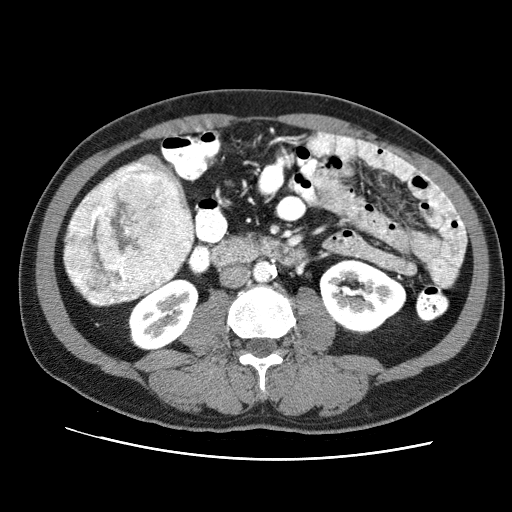
Contrast-enhanced abdominal CT (liver protocol), one axial slice. Position 17 of 71 along the scan axis. Reconstruction kernel STANDARD. Soft-tissue window (W 400 / L 40 HU). 2.5 mm slice thickness. 512 × 512 image matrix, field of view 360 × 360 mm. Case-level facts recorded for this patient, not image findings: diagnosis: hepatocellular carcinoma (patient treated with transarterial chemoembolisation; whether this scan precedes or follows treatment is not stated here); TNM stage (as recorded): Stage-II; Child-Pugh class: A.
Structures marked on this image (semi-automatically segmented with operator editing):
- liver parenchyma outside the tumour (the mass and vessels are separate outlines, so this box may not span the whole liver): bounding box <67,154,190,306> (left, top, right, bottom; pixels)
- mass: <63,165,197,305>
- liver vessels: <136,163,163,176>